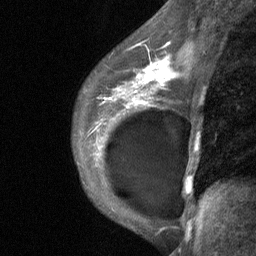
Breast MRI (dynamic contrast-enhanced), one sagittal slice. Position 45 of 64 along the scan axis. Dynamic contrast-enhanced study with each time point stored as its own series, time point 2 of 3 at this slice position (early post-contrast, ordered by acquisition time). 1.5 T. TE 4.8 ms, TR 27 ms. 2 mm slice thickness. 256 × 256 image matrix. Female patient, age 35 years. Case-level facts recorded for this patient, not image findings: setting: breast cancer imaged before/during neoadjuvant chemotherapy; receptor status: HR-positive, HER2-negative.
Annotated regions visible in this slice (semi-automatically segmented with operator editing):
- analysis volume of interest (the breast-tissue region the enhancement analysis was run in; not a lesion): bounding box [x1, y1, x2, y2] px = [74, 58, 183, 171]
- tumour enhancement mask (voxels above the 90 % enhancement threshold inside the analysis volume of interest): [132, 60, 169, 102]